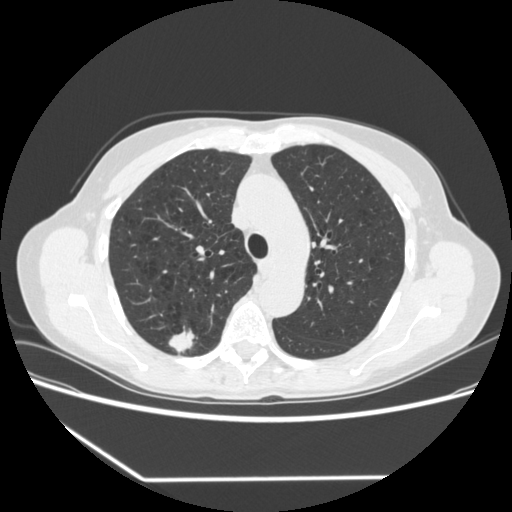
Low-dose screening chest CT, axial slice; baseline screening round; lung window (W 1500 / L -600 HU); standard (soft-tissue) reconstruction kernel (STANDARD); 120 kVp; slice 241 of 323 in the series; 512 × 512 image matrix. Female participant, aged 67 years at enrolment. Current smoker at enrolment.
Expert-annotated lung lesion, bounding box (x1, y1, x2, y2) in pixels: (156, 323, 200, 360). The screening reader recorded 2 non-calcified nodules or masses ≥4 mm on this exam (right upper lobe, right lower lobe); which of them this box marks is not recorded. Later outcome: lung cancer diagnosed 29 days after this screen — adenocarcinoma, NOS, right upper lobe, moderately differentiated (G2), stage IA (AJCC 6th edition), 24 mm at pathology.